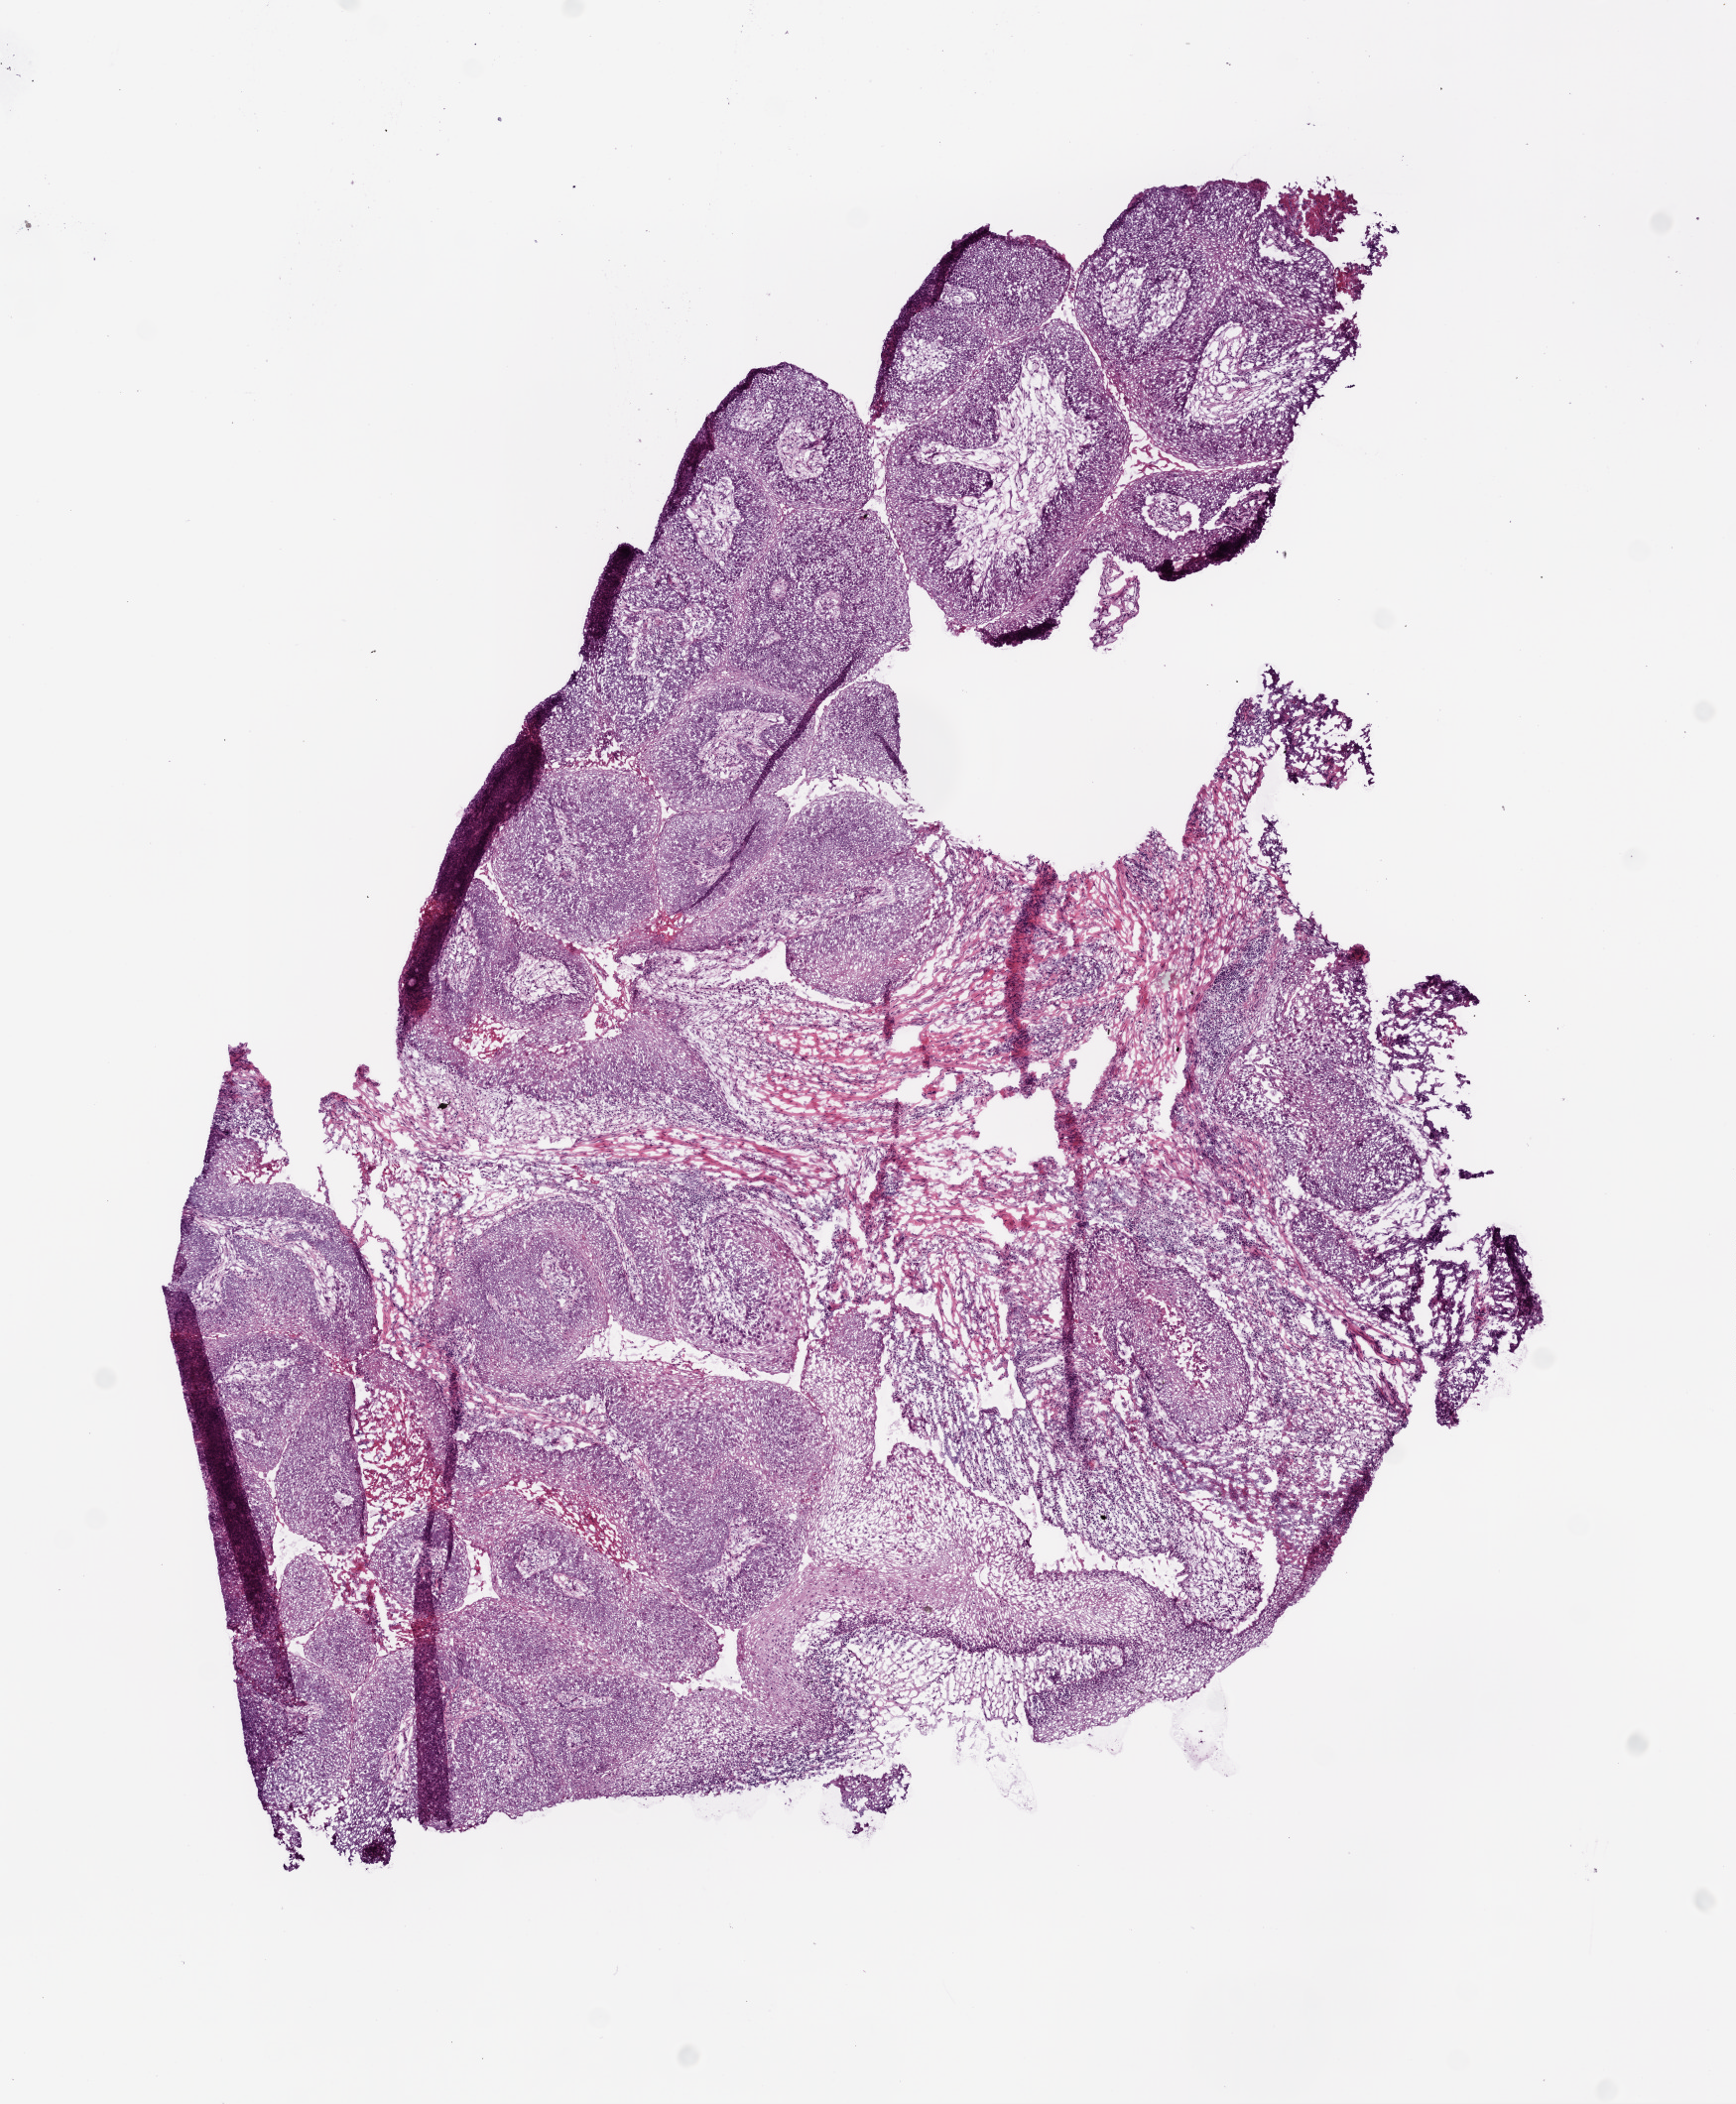
Whole-slide histology image, H&E-stained, a low-resolution overview of the entire scanned area, about 7.0 x 8.5 mm; frozen section; sample: primary tumour, head and neck. Patient: male, age at initial diagnosis 59 years. Histologic grade: G2 (moderately differentiated). Slide review estimates, as recorded: tumour cells 85%, tumour nuclei 80%, normal cells 0%, stromal cells 10%, necrosis 5%. Infiltration values recorded for this section: lymphocyte infiltration 10%, neutrophil infiltration 5%.
TNM: T3 N0. AJCC pathologic stage: III (6th edition). Lymph nodes positive (case pathology): 0 of 24 examined. Diagnosis: Squamous cell carcinoma, NOS.